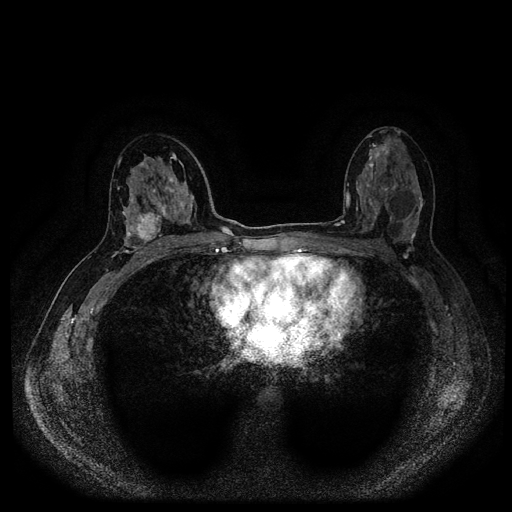
Breast MRI (dynamic contrast-enhanced, multi-phase), one axial slice; slice 56 of 116 in the series (ordered by position); dynamic contrast-enhanced series, time point 2 of 5 at this slice position (early post-contrast); 1.5 T; TE 2.6 ms, TR 5.4 ms; 512 × 512 image matrix. Patient: female, 48 years.
Annotated regions visible in this slice (semi-automatically segmented with operator editing):
- breast lesion (labelled 'tumour' in the annotation; benign lesions carry a separate 'benign' label): bounding box (x1, y1, x2, y2) in pixels: (132, 212, 163, 248)